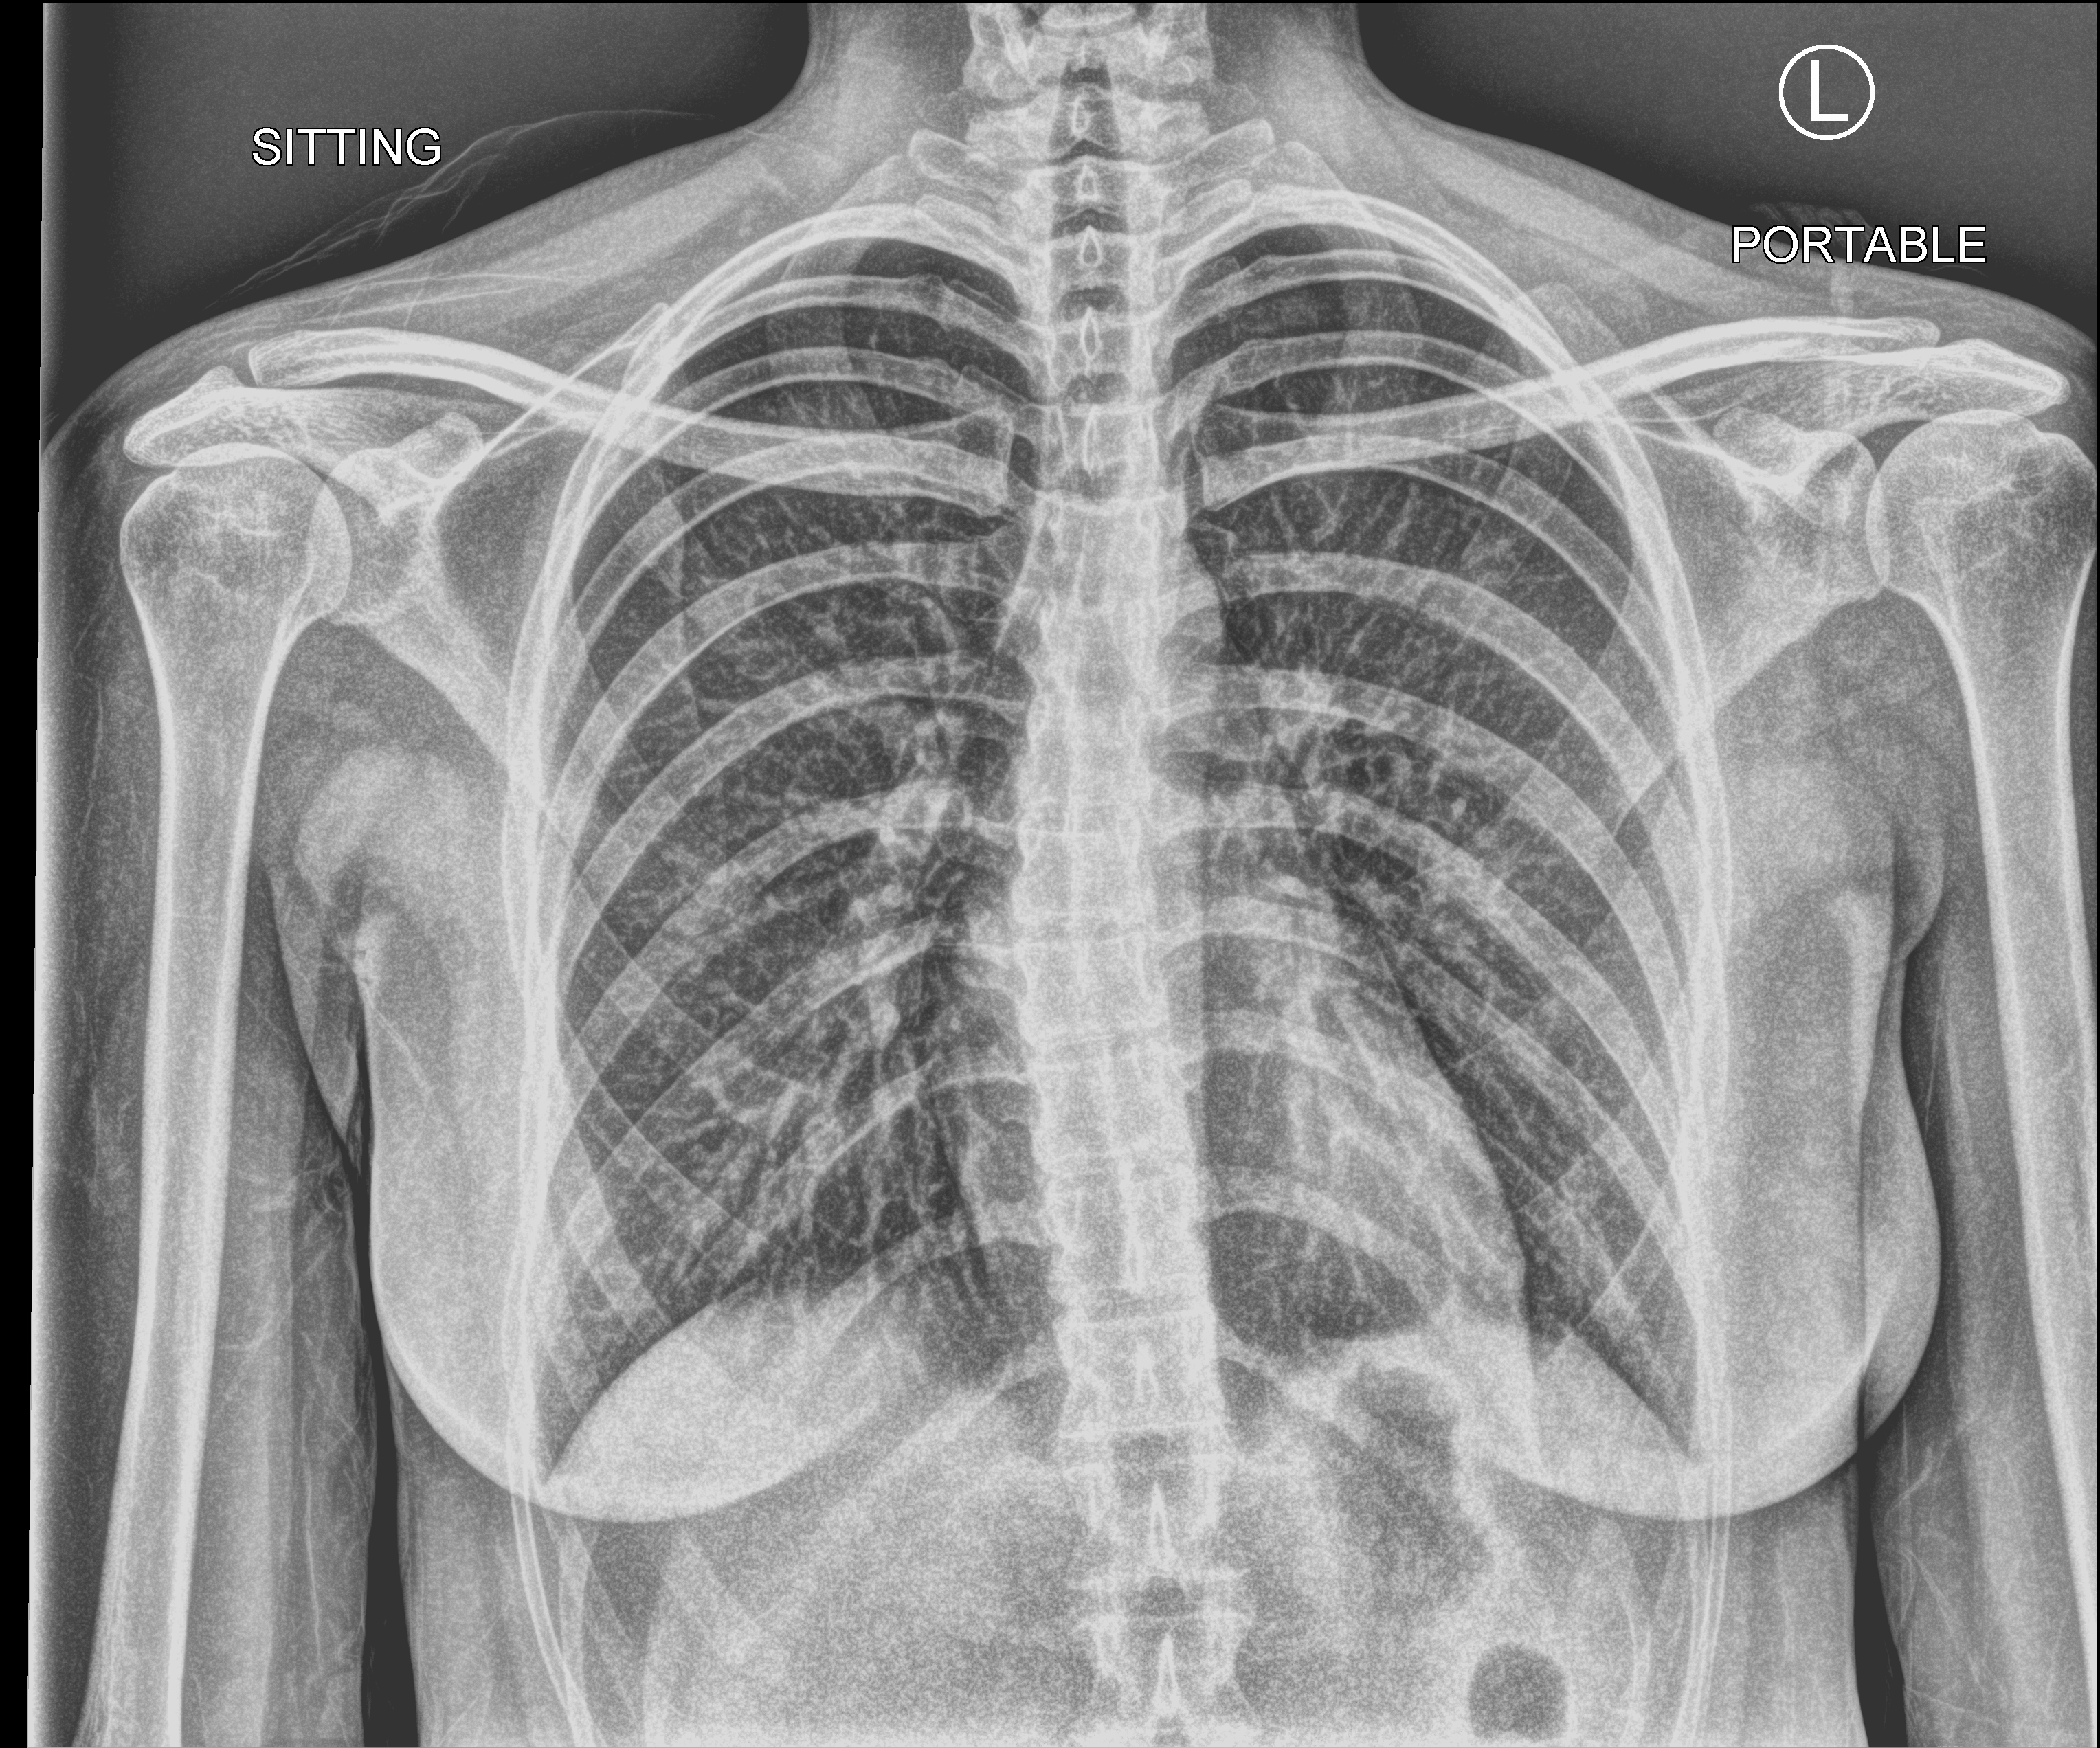
Chest X-ray (portable). Female patient hospitalised with COVID-19, age 18–59 years.
Hospital-stay facts (about this admission, not read from this image; timing relative to this image not recorded): other chronic lung disease (admission record): no.